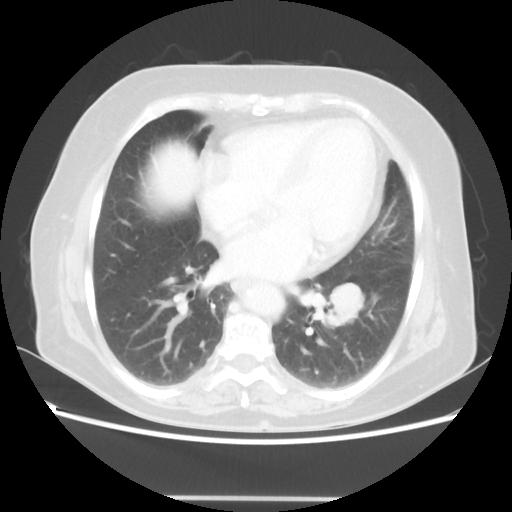
Chest CT, one axial slice. Reconstruction kernel STANDARD. Lung window (W 1500 / L -600 HU). 5 mm slice thickness. 512 × 512 image matrix. Patient: female, 73 years. Case-level facts recorded for this patient, not image findings: clinical TNM (as recorded): T1c N0 M0.
Outlined on this slice (bounding box drawn by a radiologist):
- lung tumour (recorded histology: adenocarcinoma): bounding box <326,277,366,330> (left, top, right, bottom; pixels)